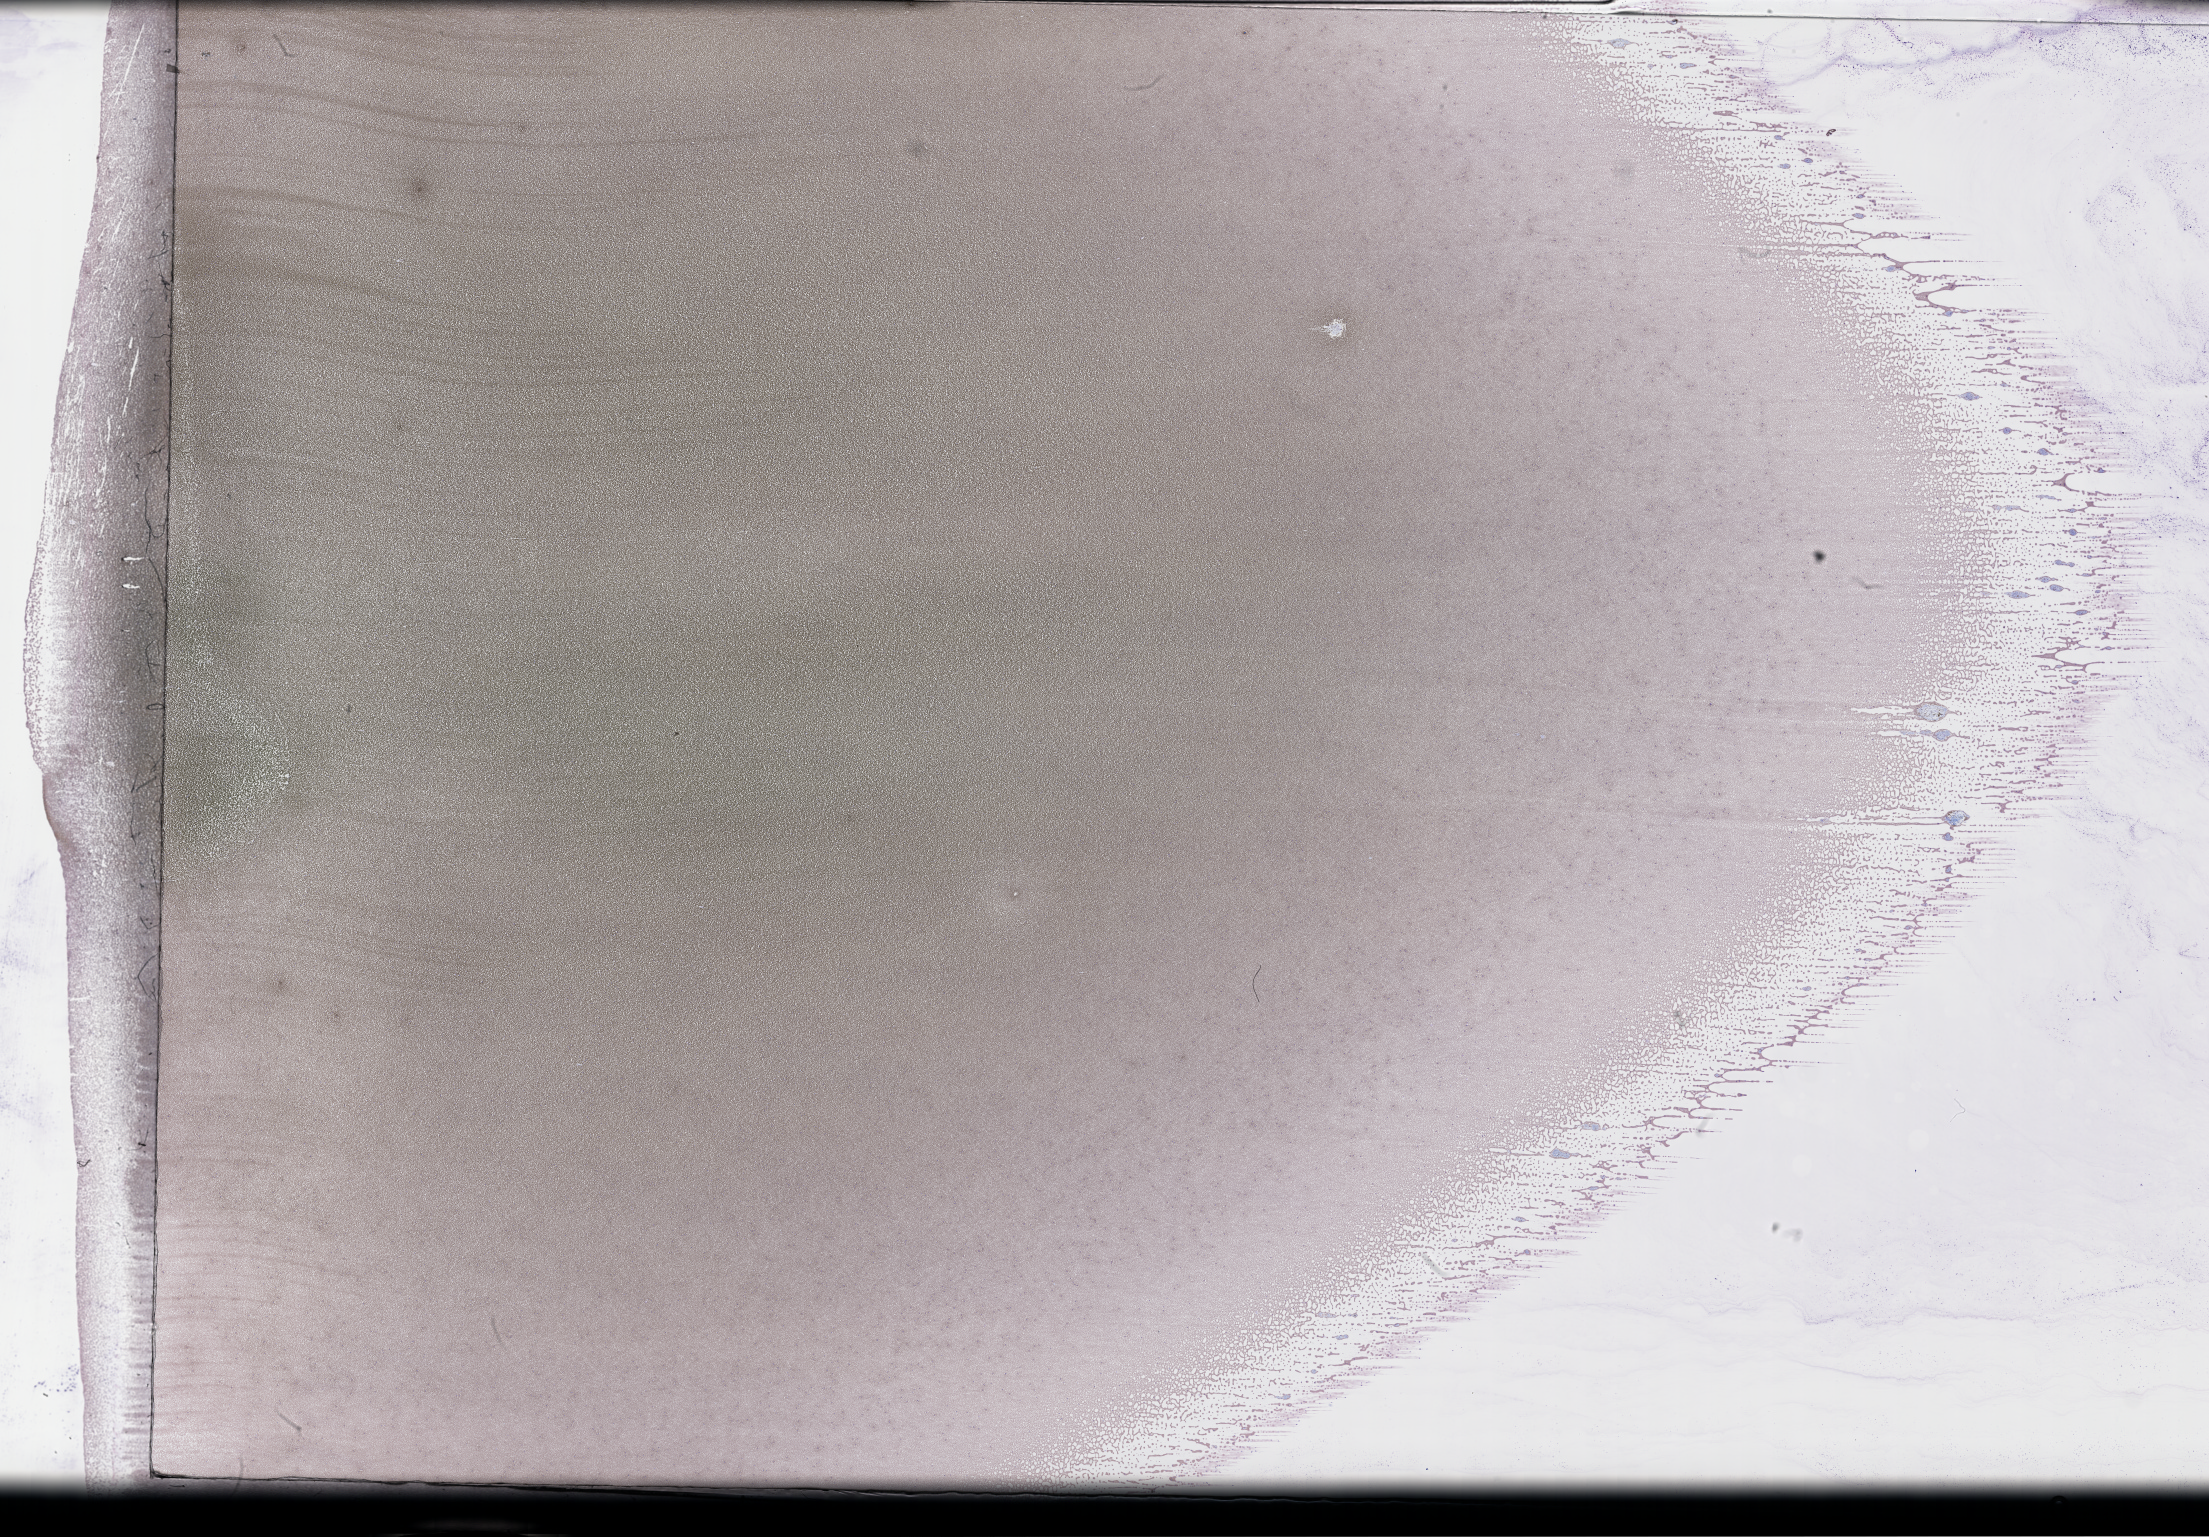
Whole-slide image of a whole blood smear, Wright–Giemsa stain, whole scanned area (about 35.7 x 24.8 mm) shown as a low-resolution overview; EDTA-anticoagulated smear. Male patient.
• from a patient with: Plasma Cell Myeloma